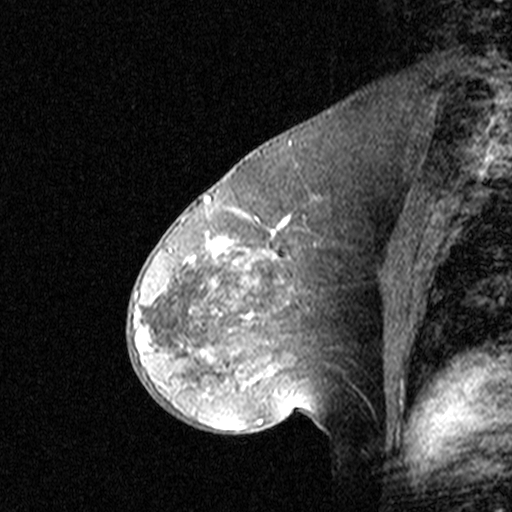
Breast MRI (dynamic contrast-enhanced), one sagittal slice. Position 22 of 44 along the scan axis. Dynamic contrast-enhanced study with each time point stored as its own series, time point 2 of 3 at this slice position (early post-contrast, ordered by acquisition time). 1.5 T. TE 4.5 ms, TR 11 ms. 512 × 512 image matrix, field of view 200 × 200 mm. Patient: female, 46 years. From the clinical record (not read from this slice): setting: breast cancer imaged before/during neoadjuvant chemotherapy; receptor status: HER2-positive.
Structures marked on this image (semi-automatically segmented with operator editing):
- analysis volume of interest (the breast-tissue region the enhancement analysis was run in; not a lesion): box from (x=144, y=172) to (x=359, y=393) px
- tumour enhancement mask (voxels above the 90 % enhancement threshold inside the analysis volume of interest): (x=144, y=196)–(x=315, y=392)